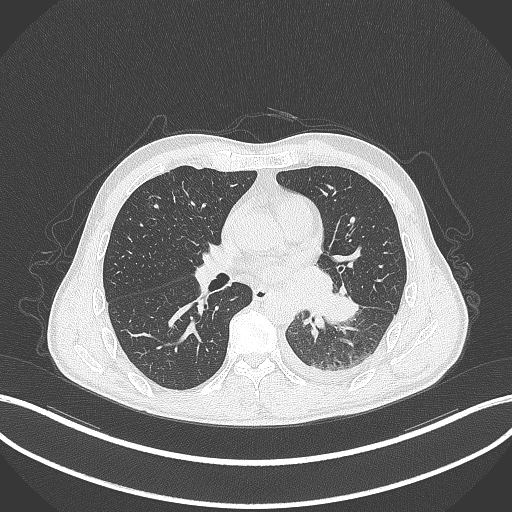
Chest CT, one axial slice. Position 161 of 295 along the scan axis. 120 kVp. Lung window (W 1500 / L -600 HU). 1 mm slice thickness. 512 × 512 image matrix, field of view 400 × 400 mm. Patient: male, 47 years. Case-level facts recorded for this patient, not image findings: clinical TNM (as recorded): T3 N1 M1c; histopathological grade: G3.
Annotated regions visible in this slice (rectangle marked by the reading radiologist):
- lung tumour (recorded histology: small cell carcinoma): bounding box [x1, y1, x2, y2] px = [313, 289, 362, 327]